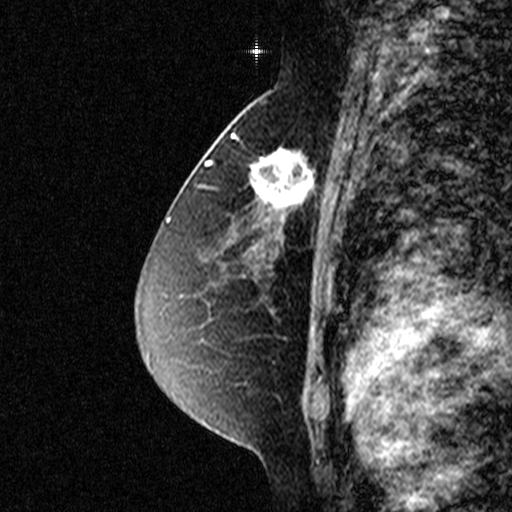
Breast MRI (dynamic contrast-enhanced), one sagittal slice; slice 26 of 44 in the series (ordered by position); dynamic contrast-enhanced study with each time point stored as its own series, time point 2 of 3 at this slice position (early post-contrast, ordered by acquisition time); 1.5 T; TE 4.5 ms, TR 11 ms; 3 mm slice thickness; 512 × 512 image matrix. Patient: female, 49 years. From the clinical record (not read from this slice): setting: breast cancer imaged before/during neoadjuvant chemotherapy; receptor status: triple-negative.
Outlined on this slice (semi-automatic segmentation, software-assisted and operator-edited):
- analysis volume of interest (the breast-tissue region the enhancement analysis was run in; not a lesion): box from (x=238, y=122) to (x=331, y=227) px
- tumour enhancement mask (voxels above the 90 % enhancement threshold inside the analysis volume of interest): (x=238, y=138)–(x=316, y=222)